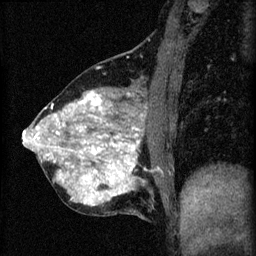
Breast MRI (dynamic contrast-enhanced), one sagittal slice. Position 23 of 60 along the scan axis. 3 images stored at this slice position (order not interpretable as contrast timing). 1.5 T. TE 4.2 ms, TR 8.2 ms. 2 mm slice thickness. 256 × 256 image matrix, field of view 180 × 180 mm. Patient: female, 40 years.
Outlined on this slice (semi-automatically segmented with operator editing):
- analysis volume of interest (the breast-tissue region the enhancement analysis was run in; not a lesion): box from (x=24, y=78) to (x=171, y=219) px
- tumour enhancement mask (voxels above the 70 % enhancement threshold inside the analysis volume of interest): (x=24, y=92)–(x=143, y=205)